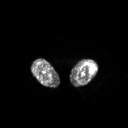
FDG PET of an extremity soft-tissue mass (from a PET/CT study), one axial slice; position 190 of 267 along the scan axis; 3.27 mm slice thickness; 128 × 128 image matrix, field of view 700 × 700 mm. Patient: female, 62 years. From the clinical record (not read from this slice): histological type: undifferentiated – high grade; grade: high; site of the primary tumour: left thigh.
Annotated regions visible in this slice (expert contour drawn on MRI and transferred to this co-registered scan by the dataset authors):
- gross tumour volume including surrounding oedema: bounding box (x1, y1, x2, y2) in pixels: (90, 67, 94, 71)